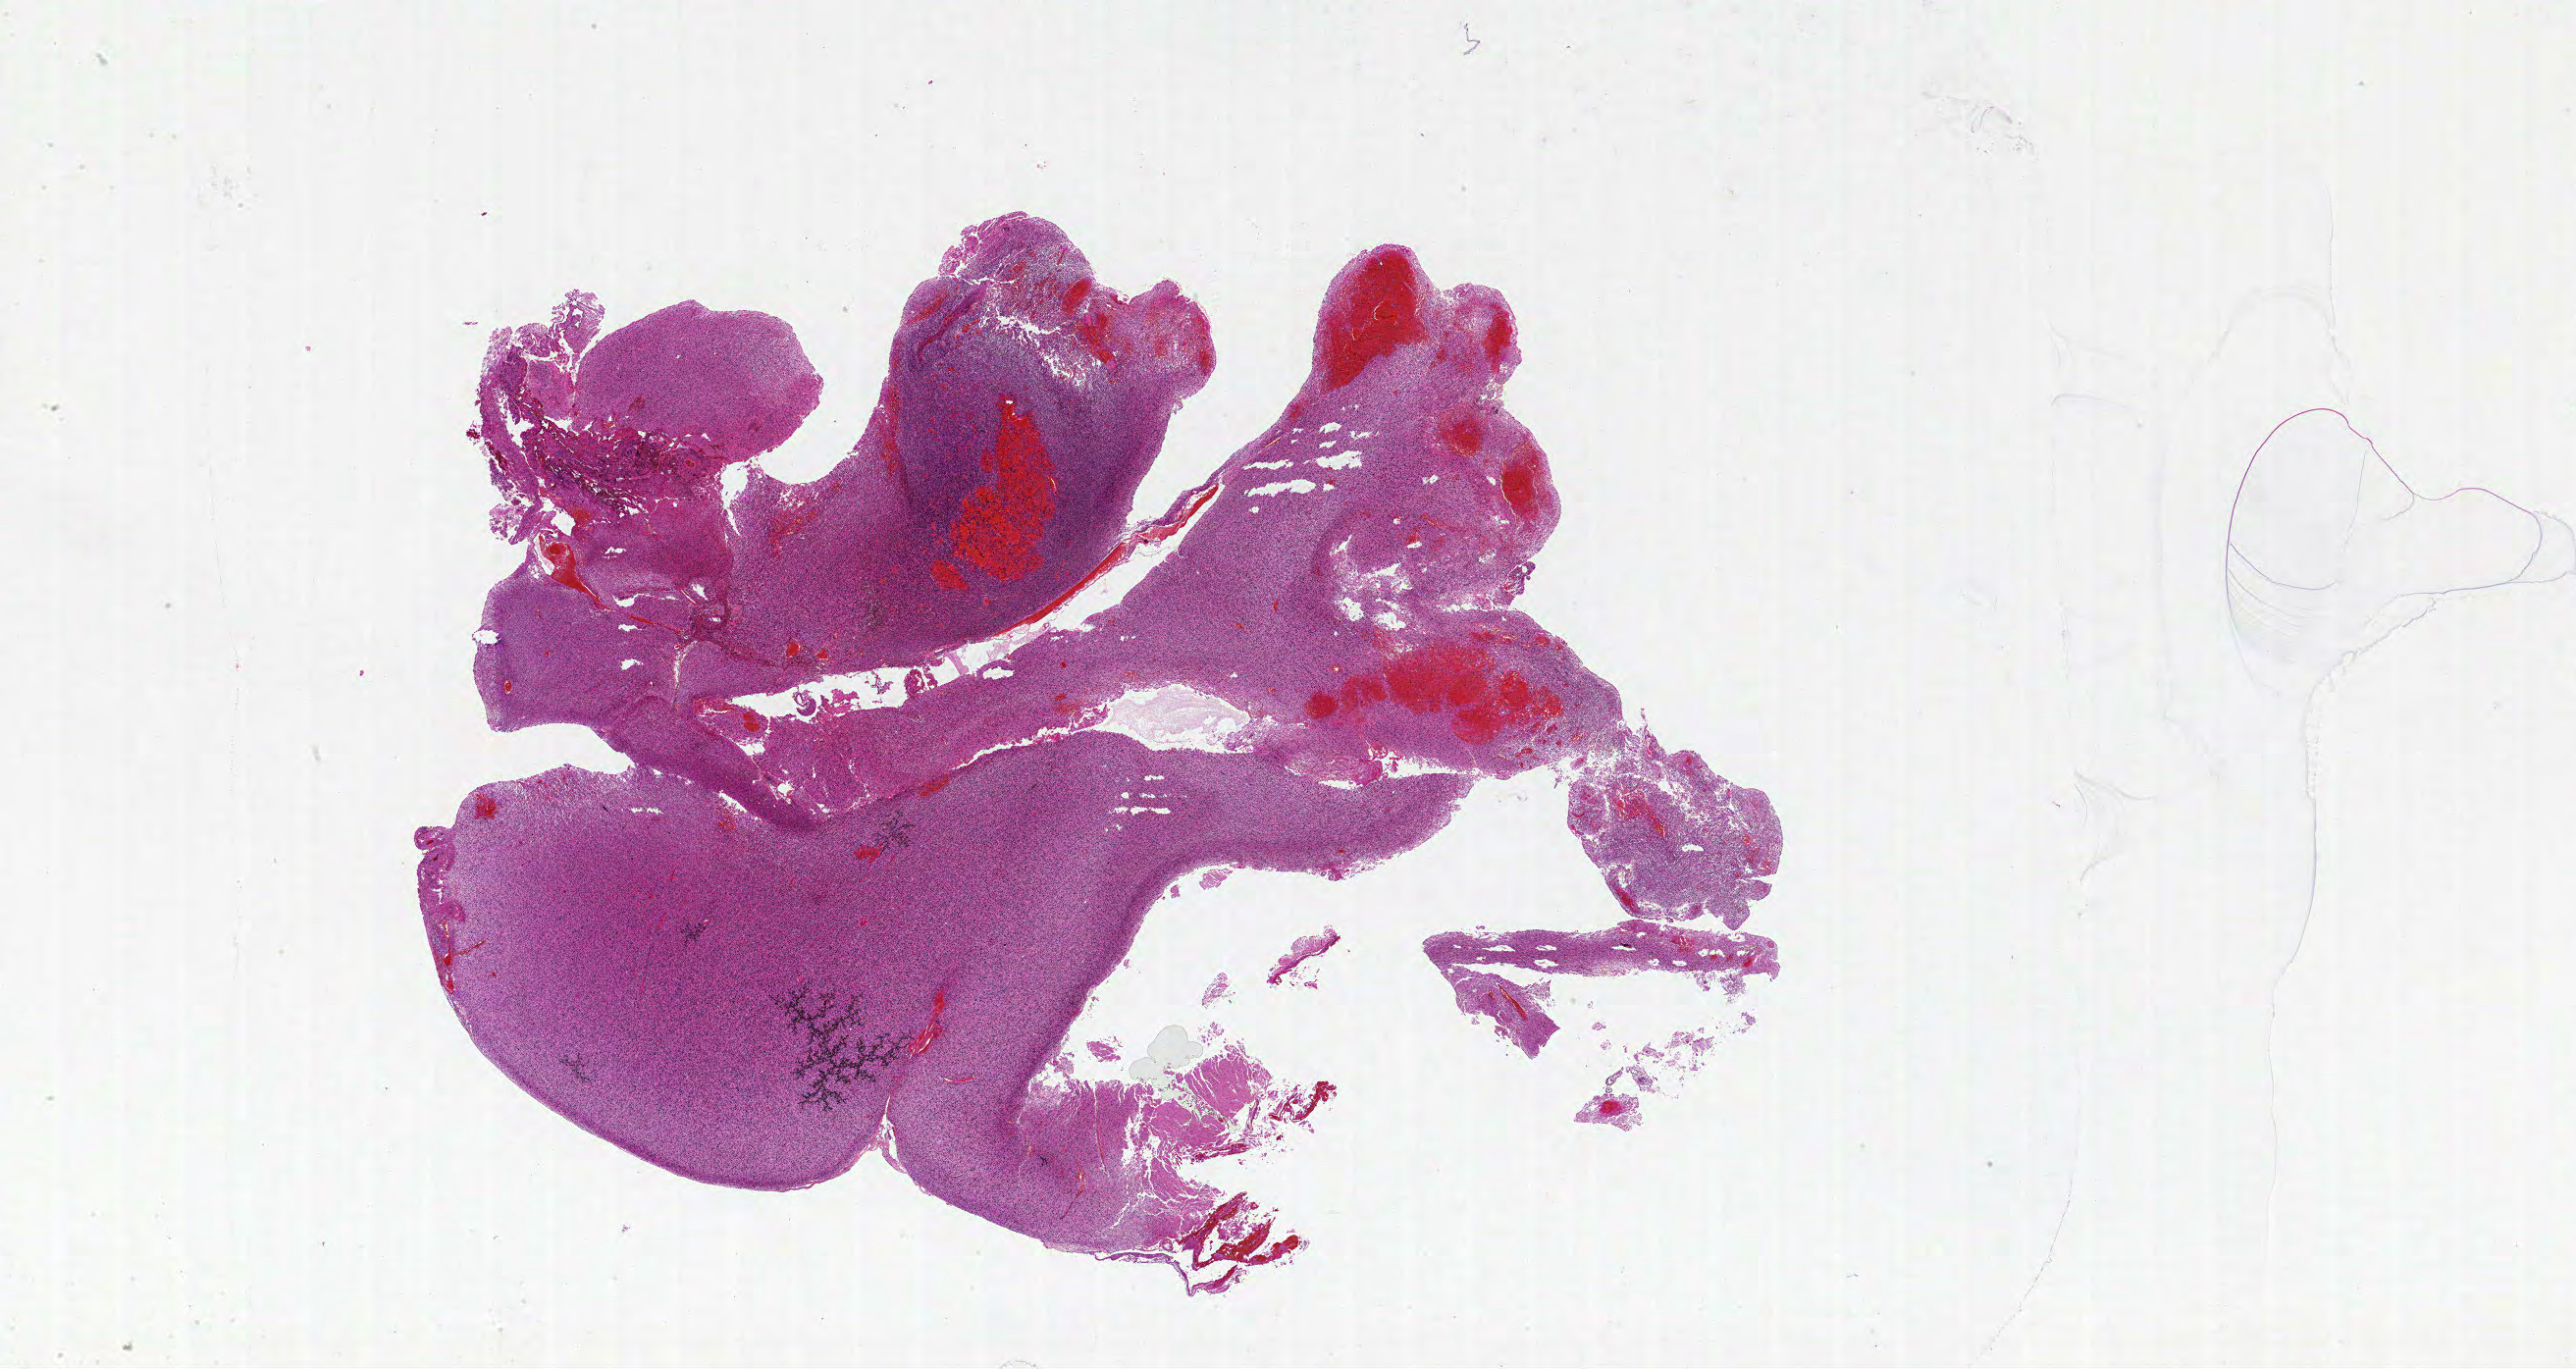
Whole-slide histology image, H&E-stained — a low-resolution overview of the entire scanned area, about 42.0 x 22.3 mm (acquisition: 20x scan), formalin-fixed paraffin-embedded (FFPE) diagnostic section, sample: primary tumour, brain. Male patient; age at initial diagnosis 55 years.
Histologic diagnosis: Glioblastoma.